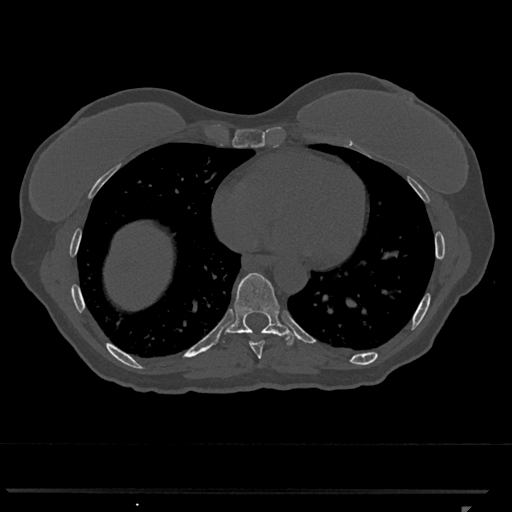
CT including the spine, one axial slice. Slice 634 of 793 in the series (ordered by position). Reconstruction kernel Br40s/3. Bone window (W 1800 / L 400 HU). 0.5 mm slice thickness. 512 × 512 image matrix, field of view 380 × 380 mm. Patient: female, 62 years. Case-level facts recorded for this patient, not image findings: primary cancer: renal.
Annotated regions visible in this slice (semi-automatically segmented with operator editing):
- T8 vertebra: bounding box (x1, y1, x2, y2) in pixels: (249, 341, 265, 359)
- T9 vertebra: (222, 273, 298, 346)